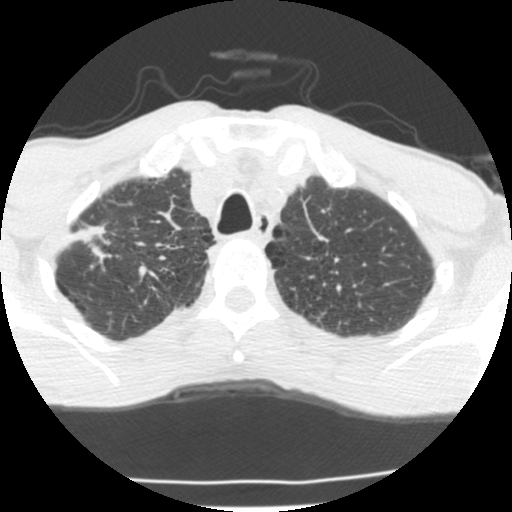
Axial slice from a low-dose chest CT screening exam. Second annual screen. Lung window (W 1500 / L -600 HU). 512 × 512 image matrix, field of view 283 × 283 mm. Male participant, aged 62 years at enrolment.
• Expert reader's lesion annotation, bounding box [x1, y1, x2, y2] px = [53, 215, 130, 271].
• Reader record for this screening exam (exam-level; its link to the box is not recorded): non-calcified nodule or mass ≥4 mm, right upper lobe, 23 × 11 mm, spiculated (stellate) margins, soft tissue attenuation, pre-existing on the prior screen: yes.
• Official screen result: positive, change unspecified: nodule(s) >= 4 mm or enlarging nodule(s), mass(es), or other non-specific abnormalities suspicious for lung cancer.
• Later outcome: lung cancer diagnosed 277 days after this screen — adenocarcinoma, NOS, right upper lobe, poorly differentiated (G3), stage IIA (AJCC 6th edition), 22 mm at pathology.